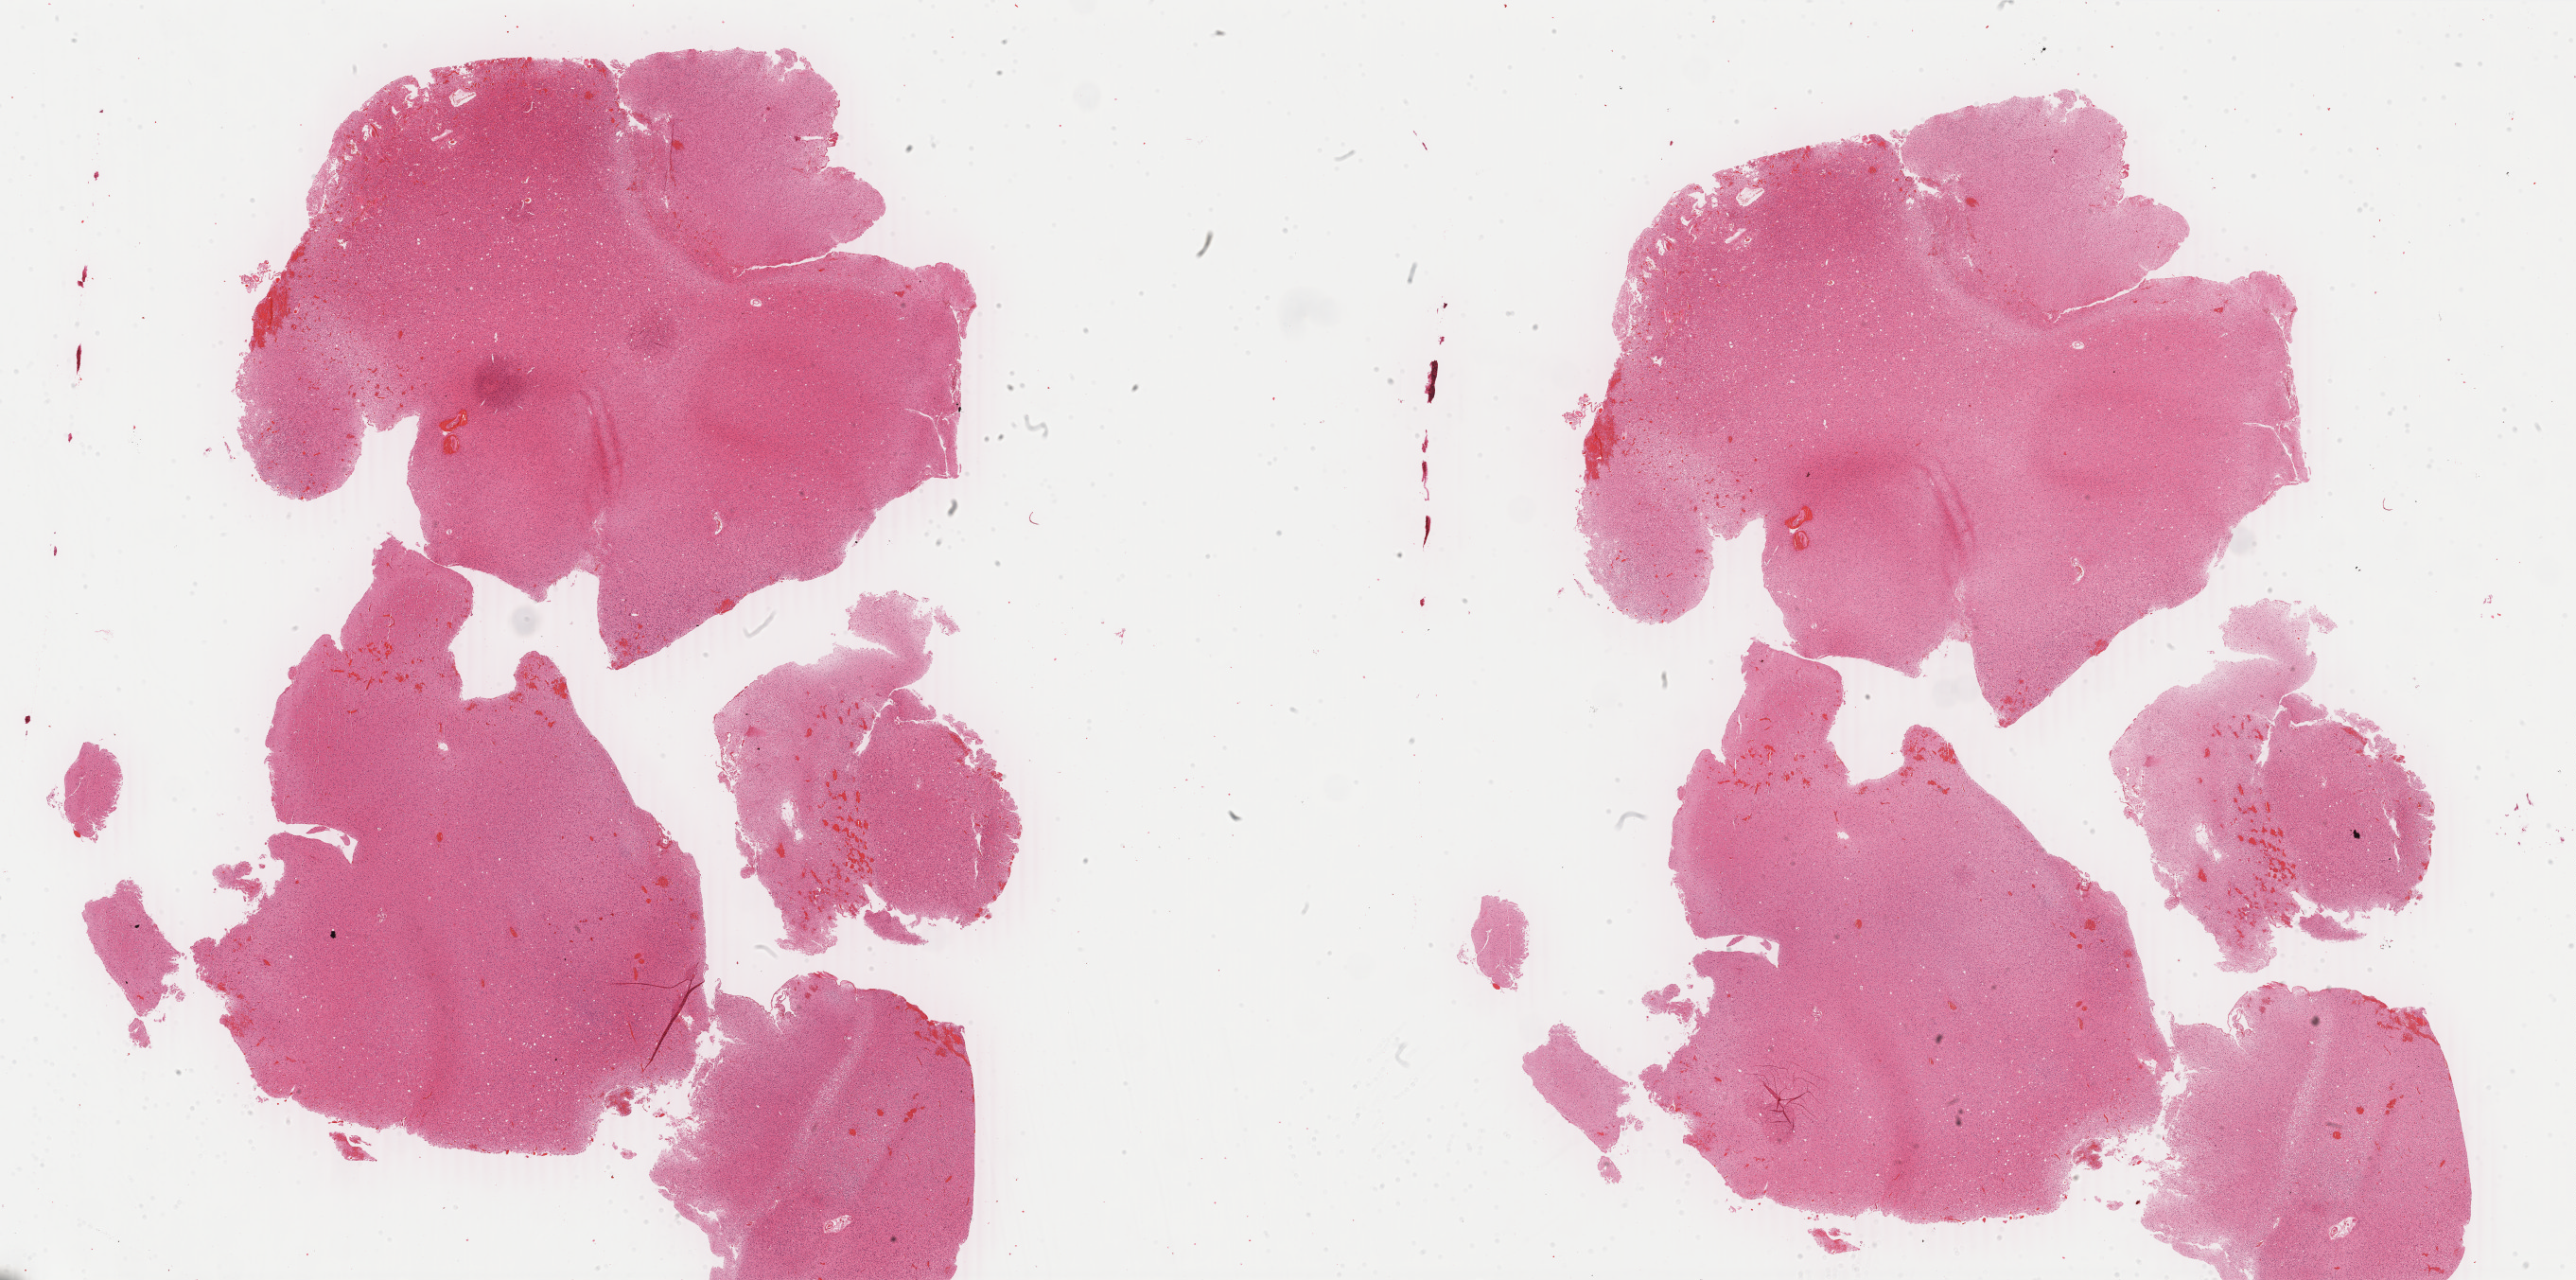
Digitized H&E-stained tissue section (whole slide), low-resolution overview of the scanned area, about 43.3 x 21.5 mm. Formalin-fixed paraffin-embedded (FFPE) diagnostic section. Primary tumour sample from the brain. Patient: female, age at initial diagnosis 41 years. Histologic grade: G2 (moderately differentiated).
Diagnosis: Astrocytoma, NOS (cerebrum). Laterality: right.